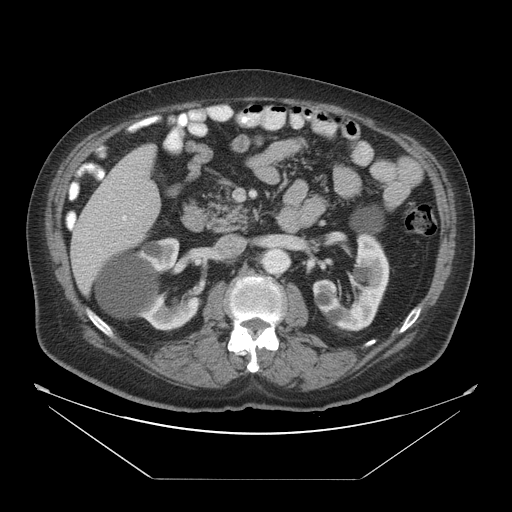
Contrast-enhanced abdominal CT, one axial slice; position 20 of 45 along the scan axis; reconstruction kernel STANDARD; 120 kVp; soft-tissue window (W 400 / L 40 HU); 512 × 512 image matrix, field of view 463 × 463 mm. Male patient, age 87 years. From the clinical record (not read from this slice): diagnosis: colorectal cancer liver metastases, imaged before liver resection; multiple liver metastases: no; largest metastasis: 4.5 cm.
Outlined on this slice (expert manual segmentation):
- liver: box from (x=70, y=142) to (x=162, y=297) px
- portal vein (with intrahepatic branches): (x=123, y=181)–(x=135, y=220)